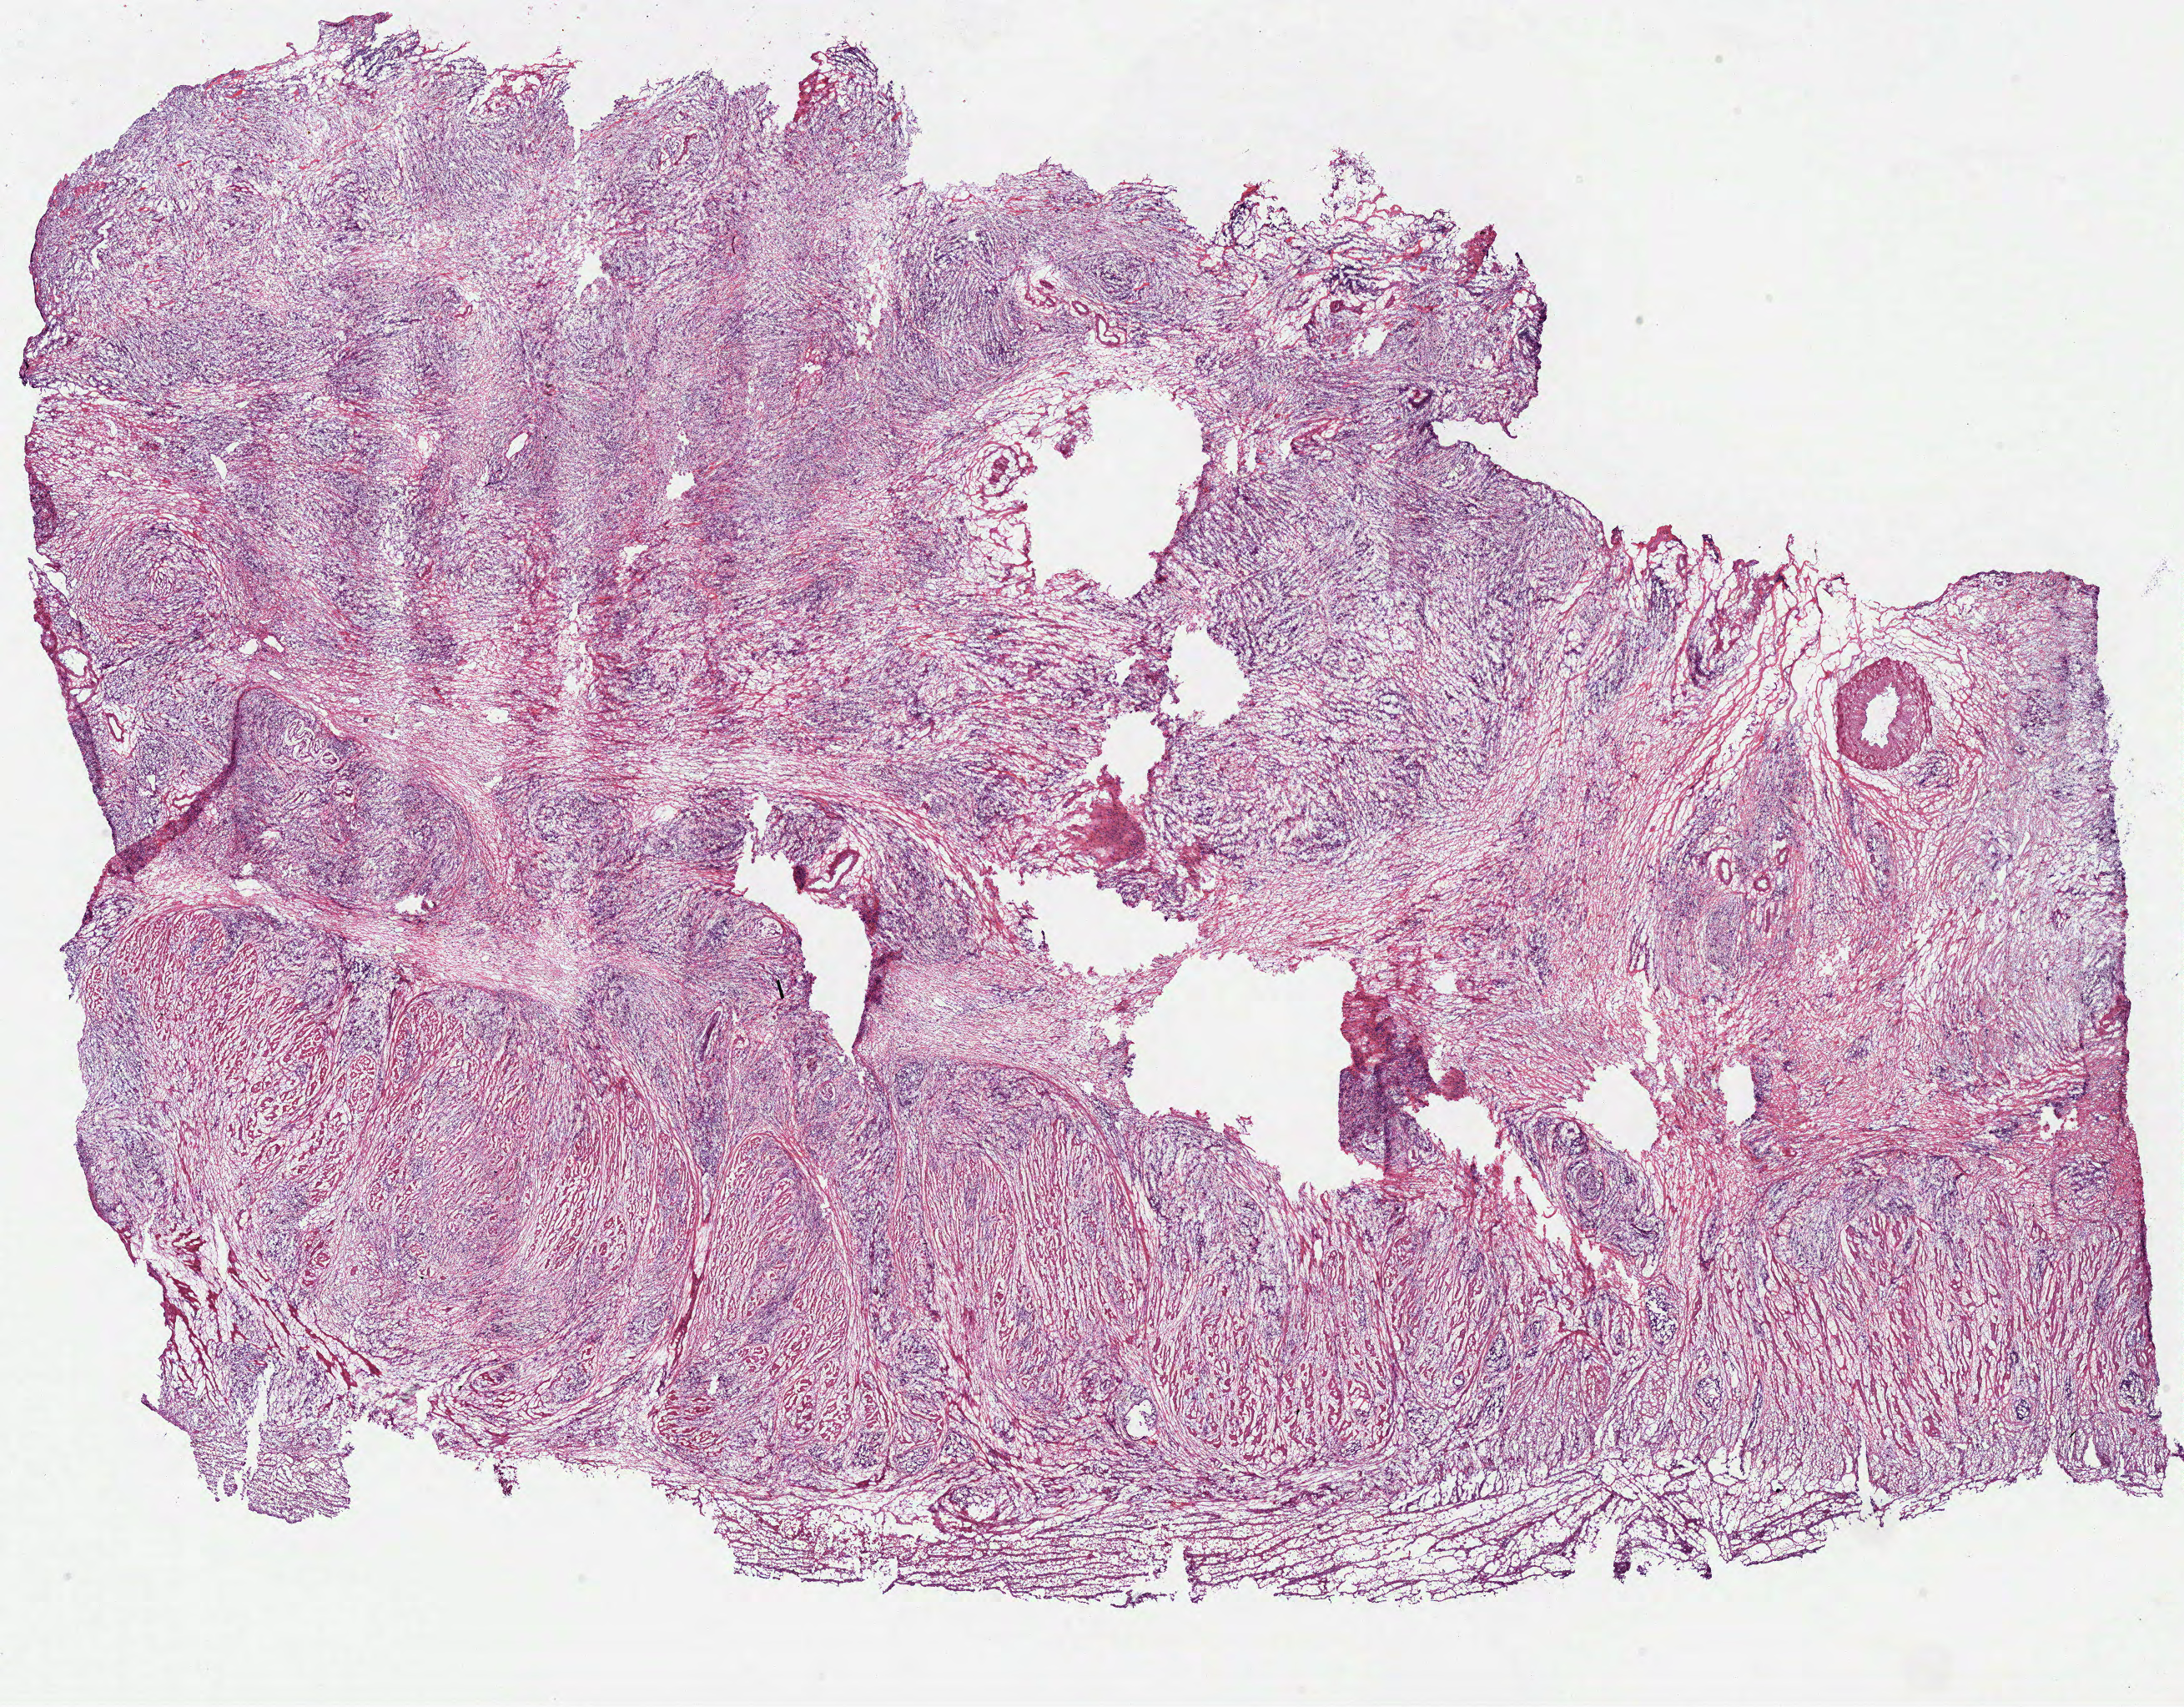
H&E whole-slide image, whole scanned area (about 20.6 x 16.1 mm, from a 40x scan) shown as a low-resolution overview; frozen section from the top of the tissue portion; sample: primary tumour, stomach. Male, age 64 years at initial diagnosis. Histologic grade: G3 (poorly differentiated). Pathologist review of this section (percent, as recorded): tumour cells 80%, tumour nuclei 60%, normal cells 0%, stromal cells 20%, necrosis 0%. Infiltration values recorded for this section: lymphocyte infiltration 20%, monocyte infiltration 5%, neutrophil infiltration 5%.
Lymph nodes positive (case pathology): 11 of 15 examined. Diagnosis: Adenocarcinoma, NOS (cardia, NOS). AJCC pathologic stage: IV (7th edition).